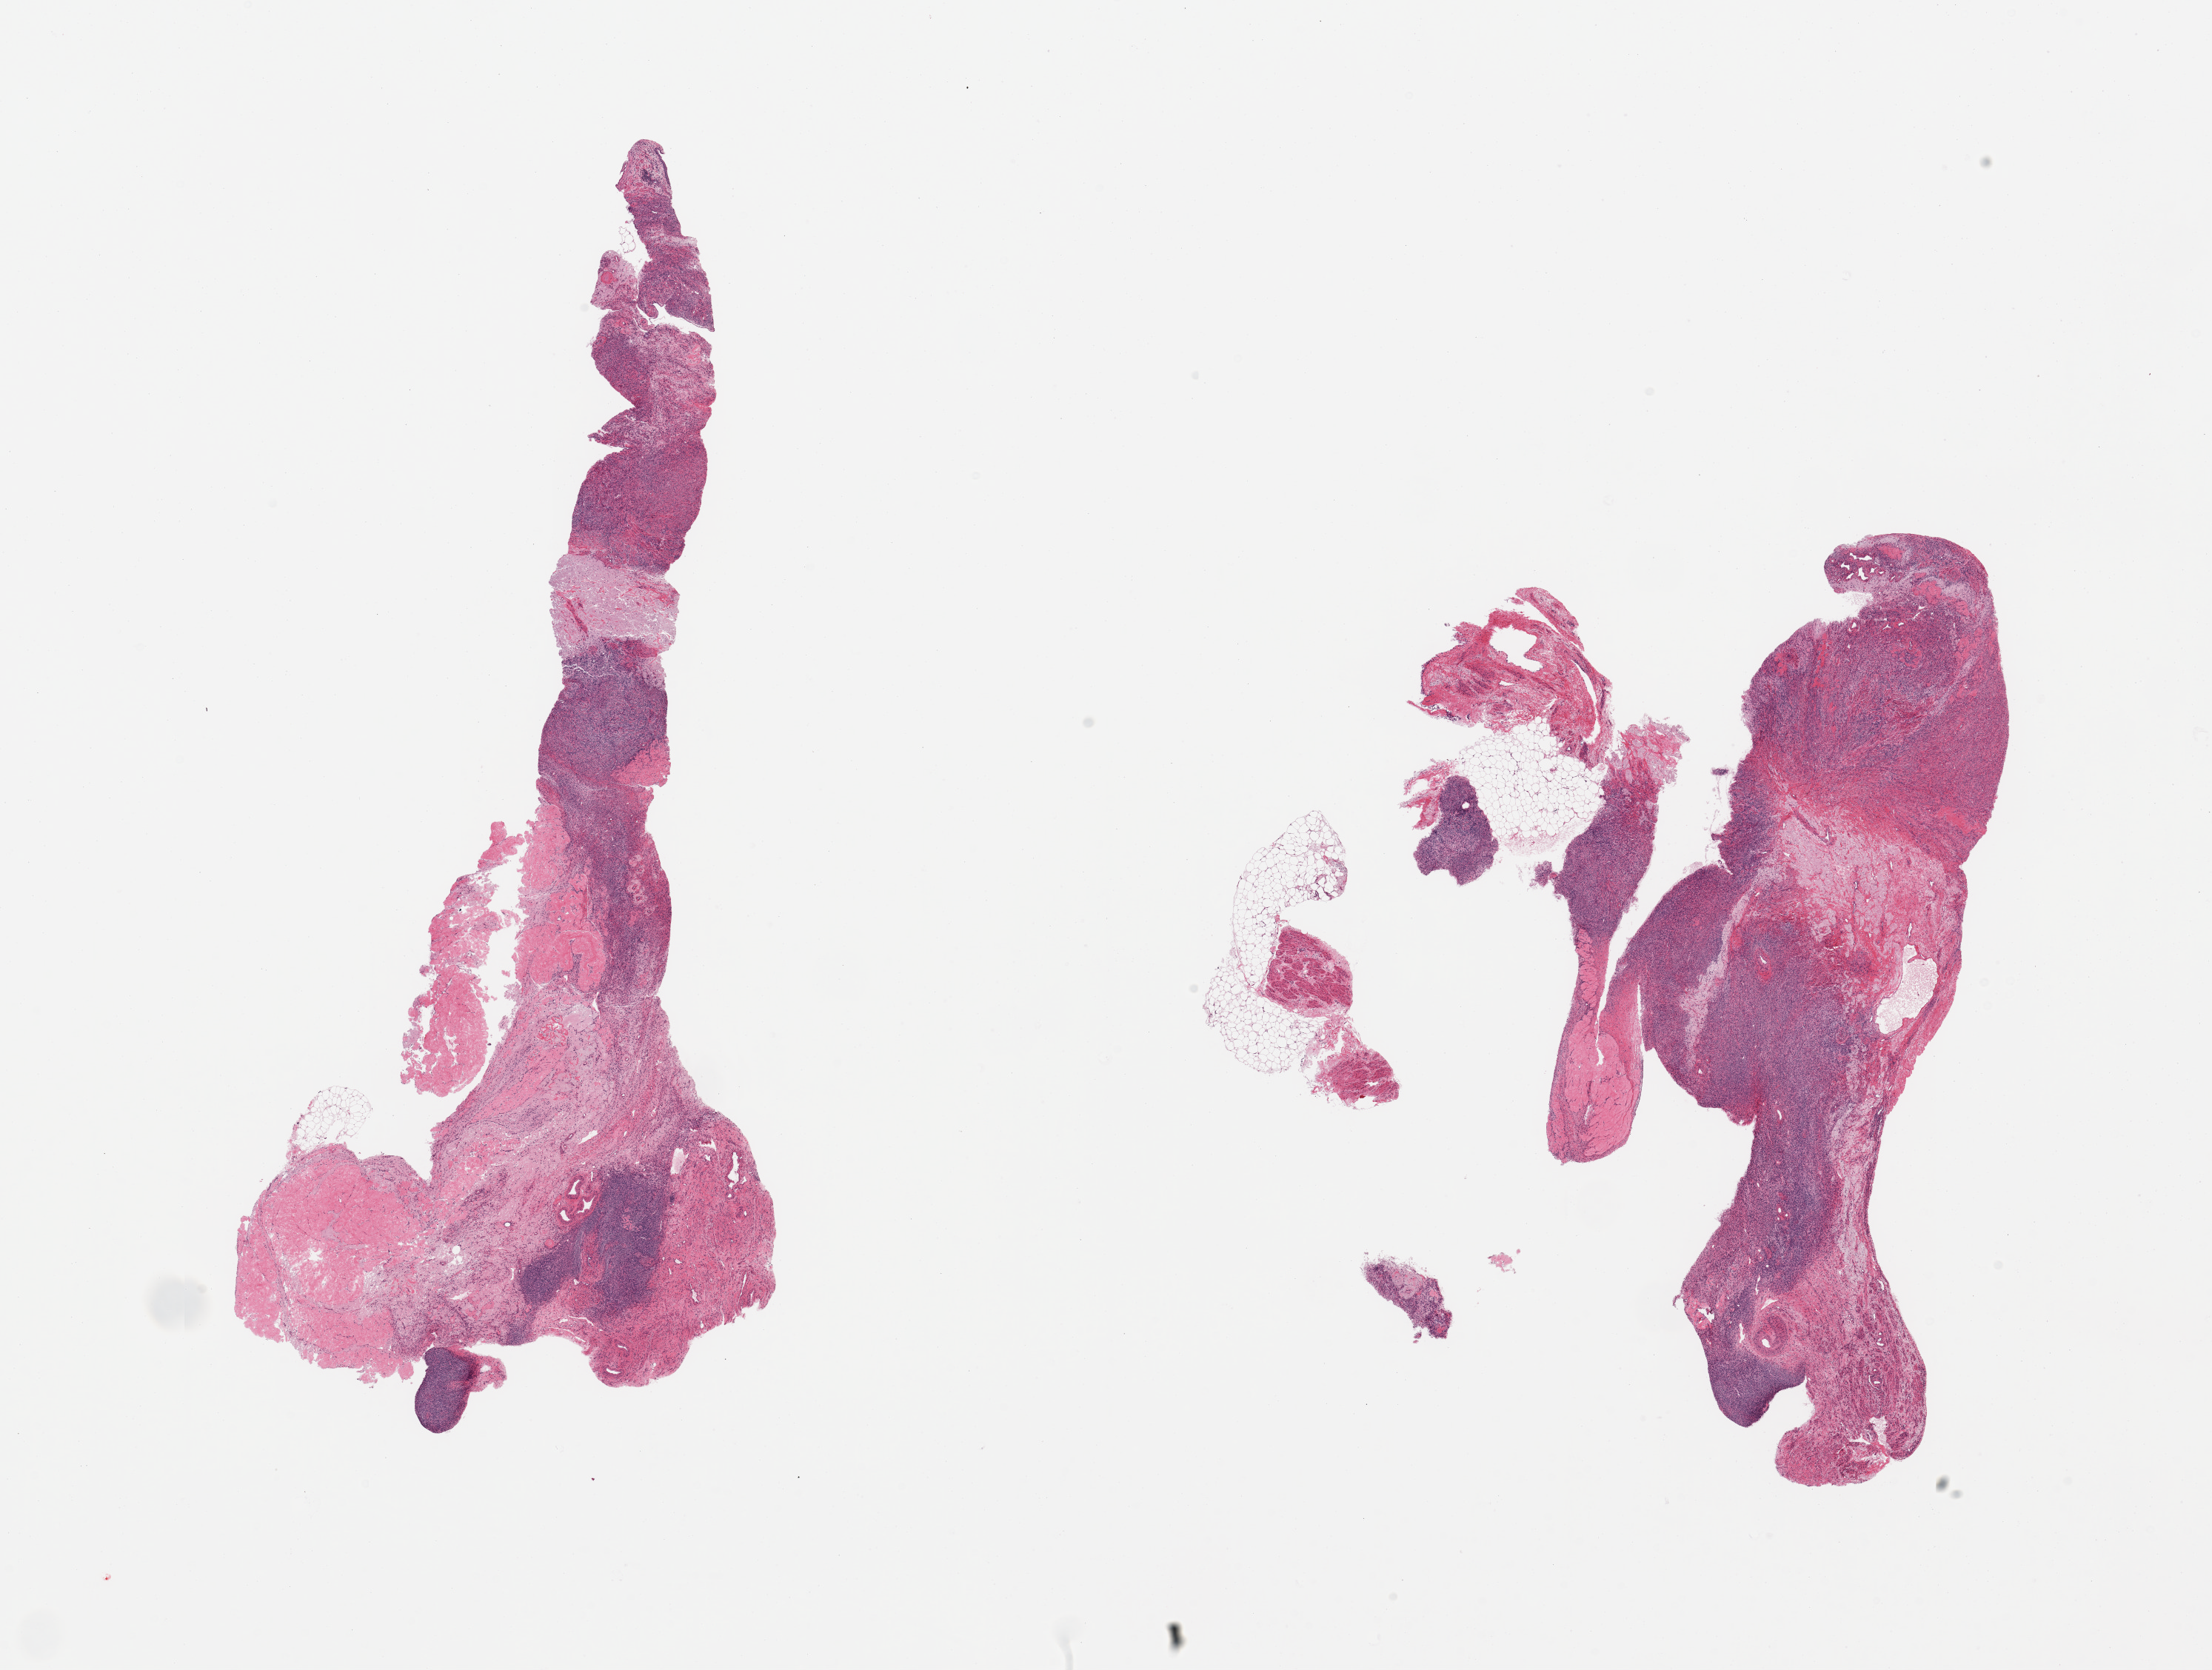
Digitized H&E-stained section, shown as a low-resolution overview of the whole scanned area (about 23.6 x 17.8 mm); PAXgene-fixed, paraffin-embedded tissue; target tissue: ovary; tissue donor sample. Donor sex: female.
Review note (as recorded): 2 pieces, typical post menopausal cortex.